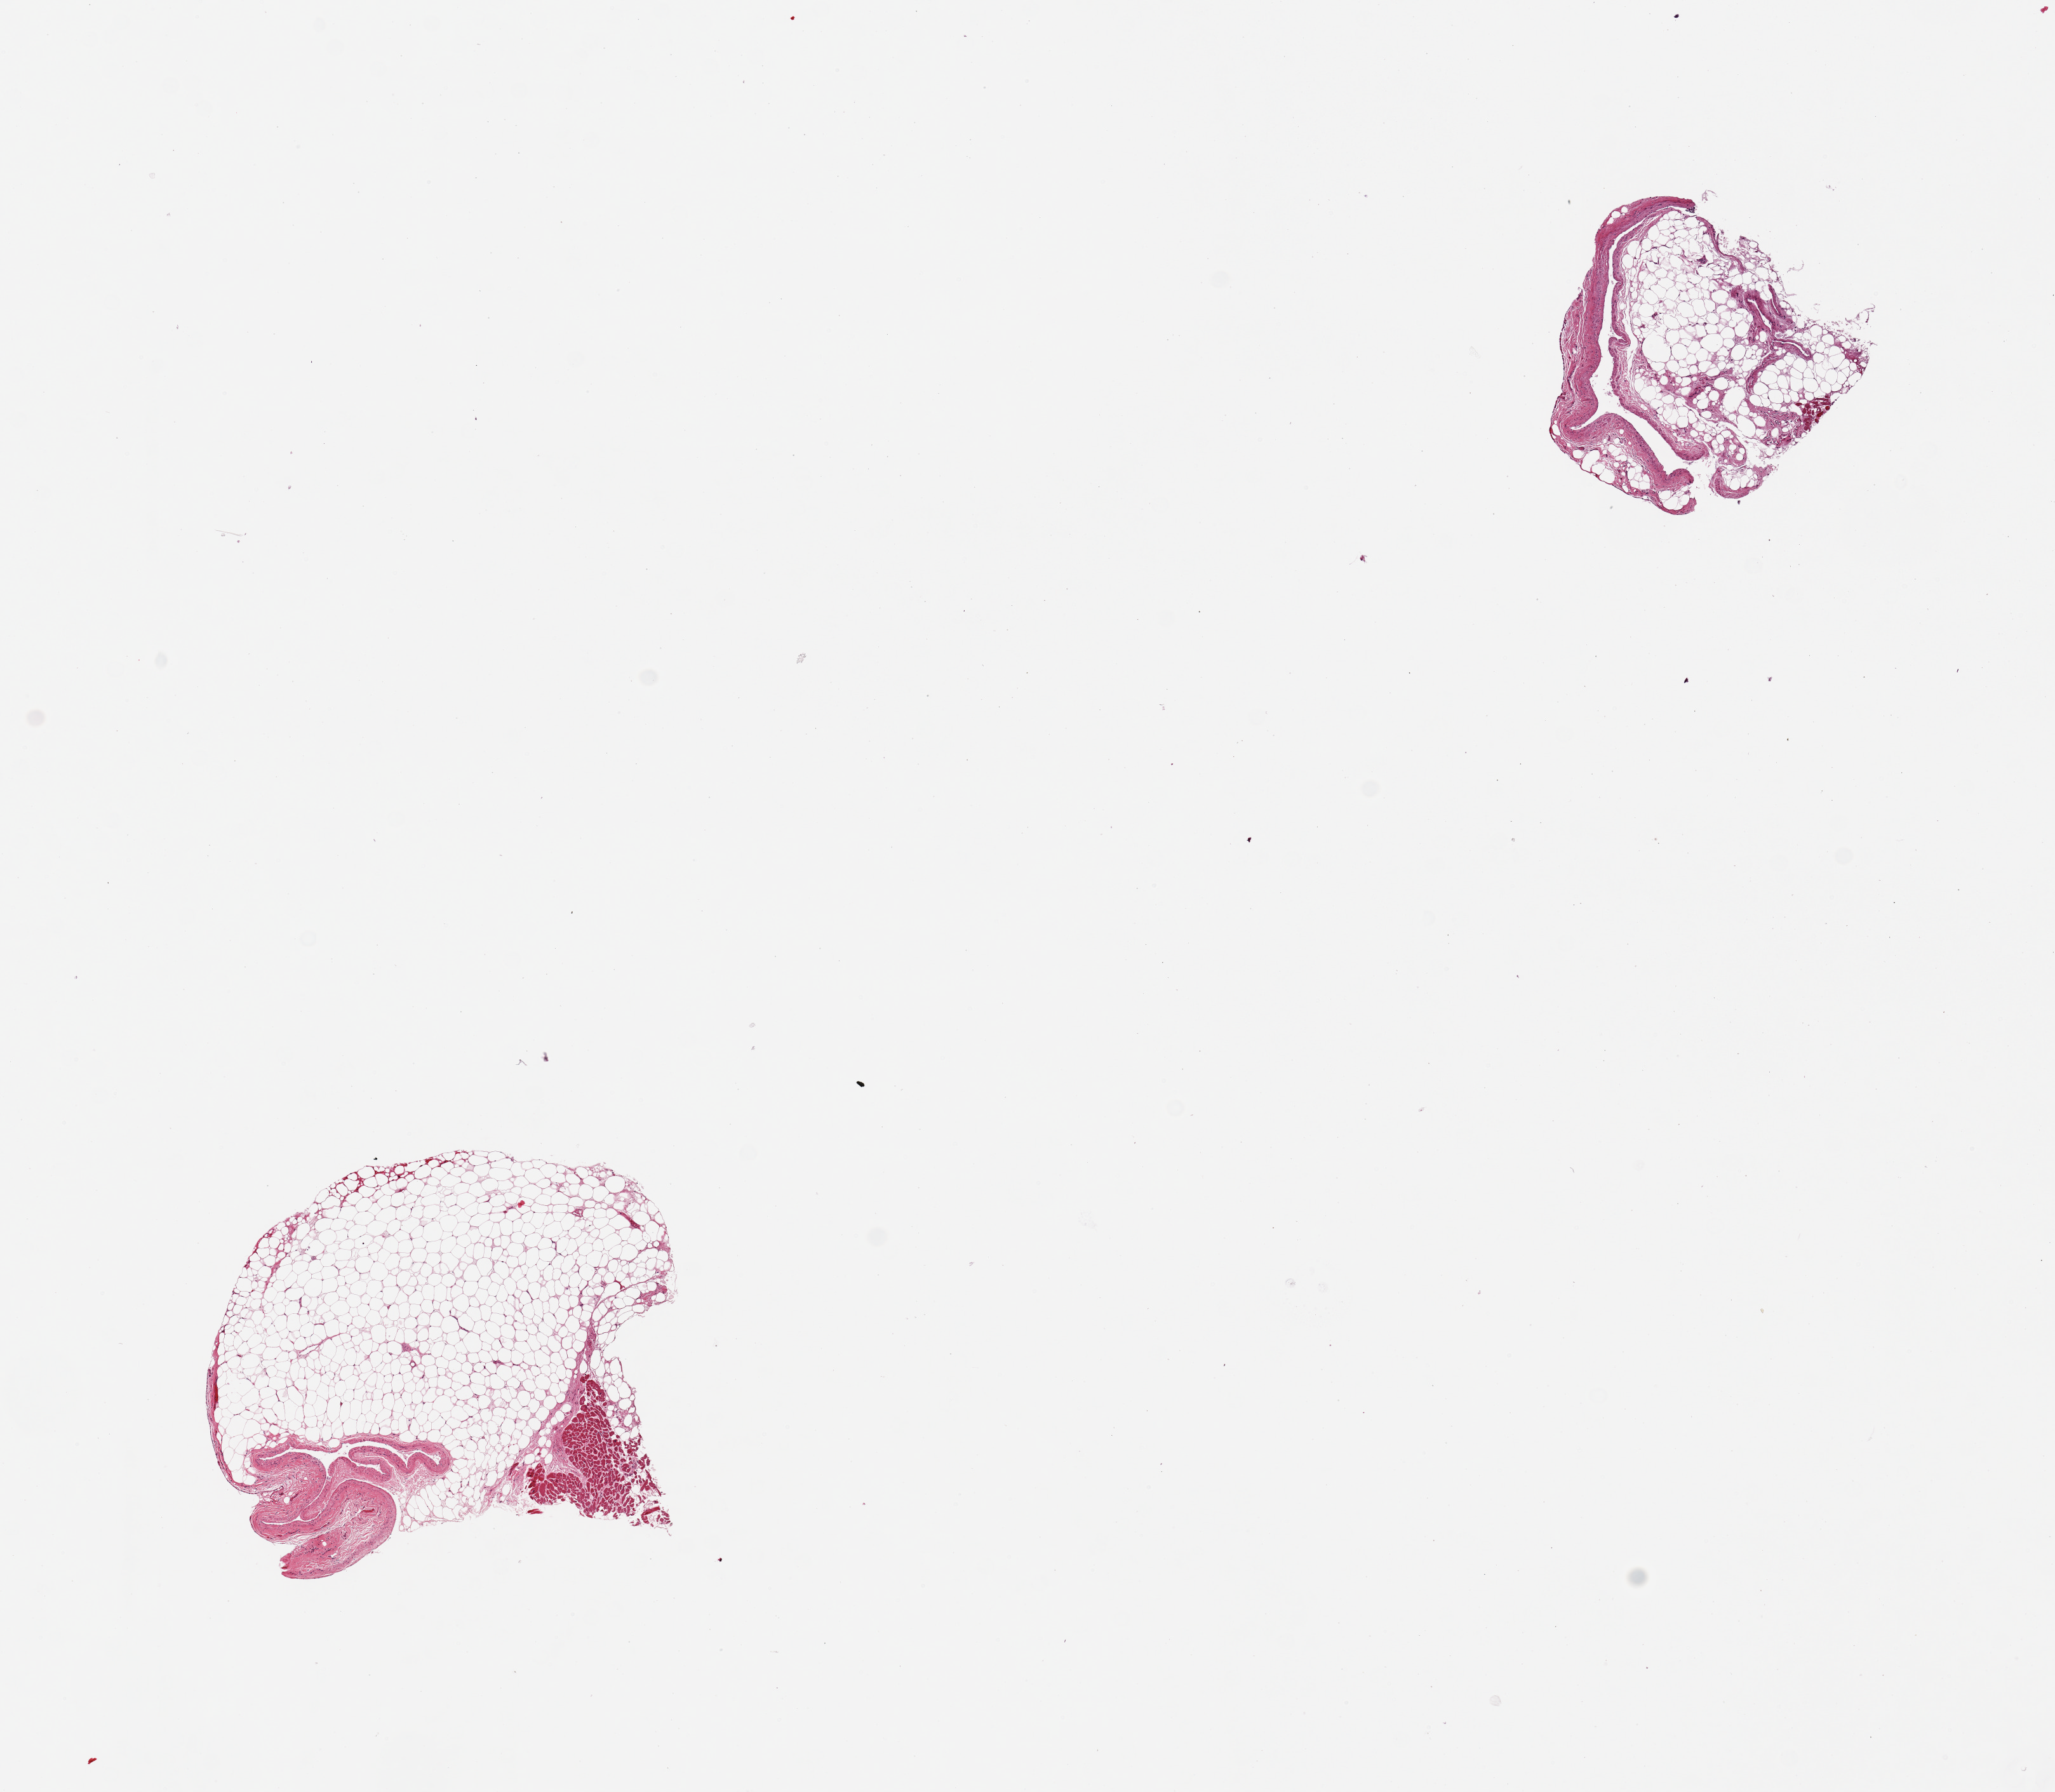
Digitized hematoxylin and eosin (H&E)-stained section, shown as a low-resolution overview of the whole scanned area (about 12.8 x 11.2 mm); PAXgene-fixed paraffin-embedded (PFPE) section; target tissue: coronary artery; tissue donor sample.
Reviewer comment on this tissue sample: 2 pieces, minute, ~1mm arteries; abundant adherent fat, up to ~2mm,on both.